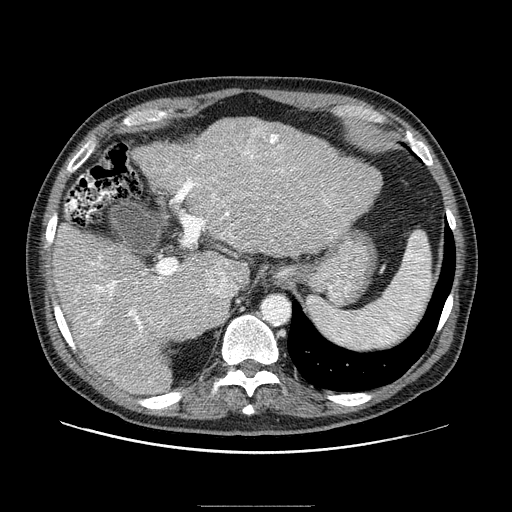
Contrast-enhanced abdominal CT (liver protocol), one axial slice; slice 60 of 99 in the series (ordered by position); reconstruction kernel STANDARD; one of 2 acquisitions stored at this slice position; soft-tissue window (W 400 / L 40 HU); 512 × 512 image matrix. From the clinical record (not read from this slice): diagnosis: hepatocellular carcinoma (patient treated with transarterial chemoembolisation; whether this scan precedes or follows treatment is not stated here); TNM stage (as recorded): Stage-II; Child-Pugh class: A; tumour nodularity: multinodular; tumour size: 3.2 cm.
Outlined on this slice (semi-automatically segmented with operator editing):
- abdominal aorta: bounding box (x1, y1, x2, y2) in pixels: (263, 296, 290, 324)
- liver parenchyma outside the tumour (the mass and vessels are separate outlines, so this box may not span the whole liver): (52, 118, 381, 394)
- mass: (241, 127, 290, 172)
- liver vessels: (74, 155, 332, 339)